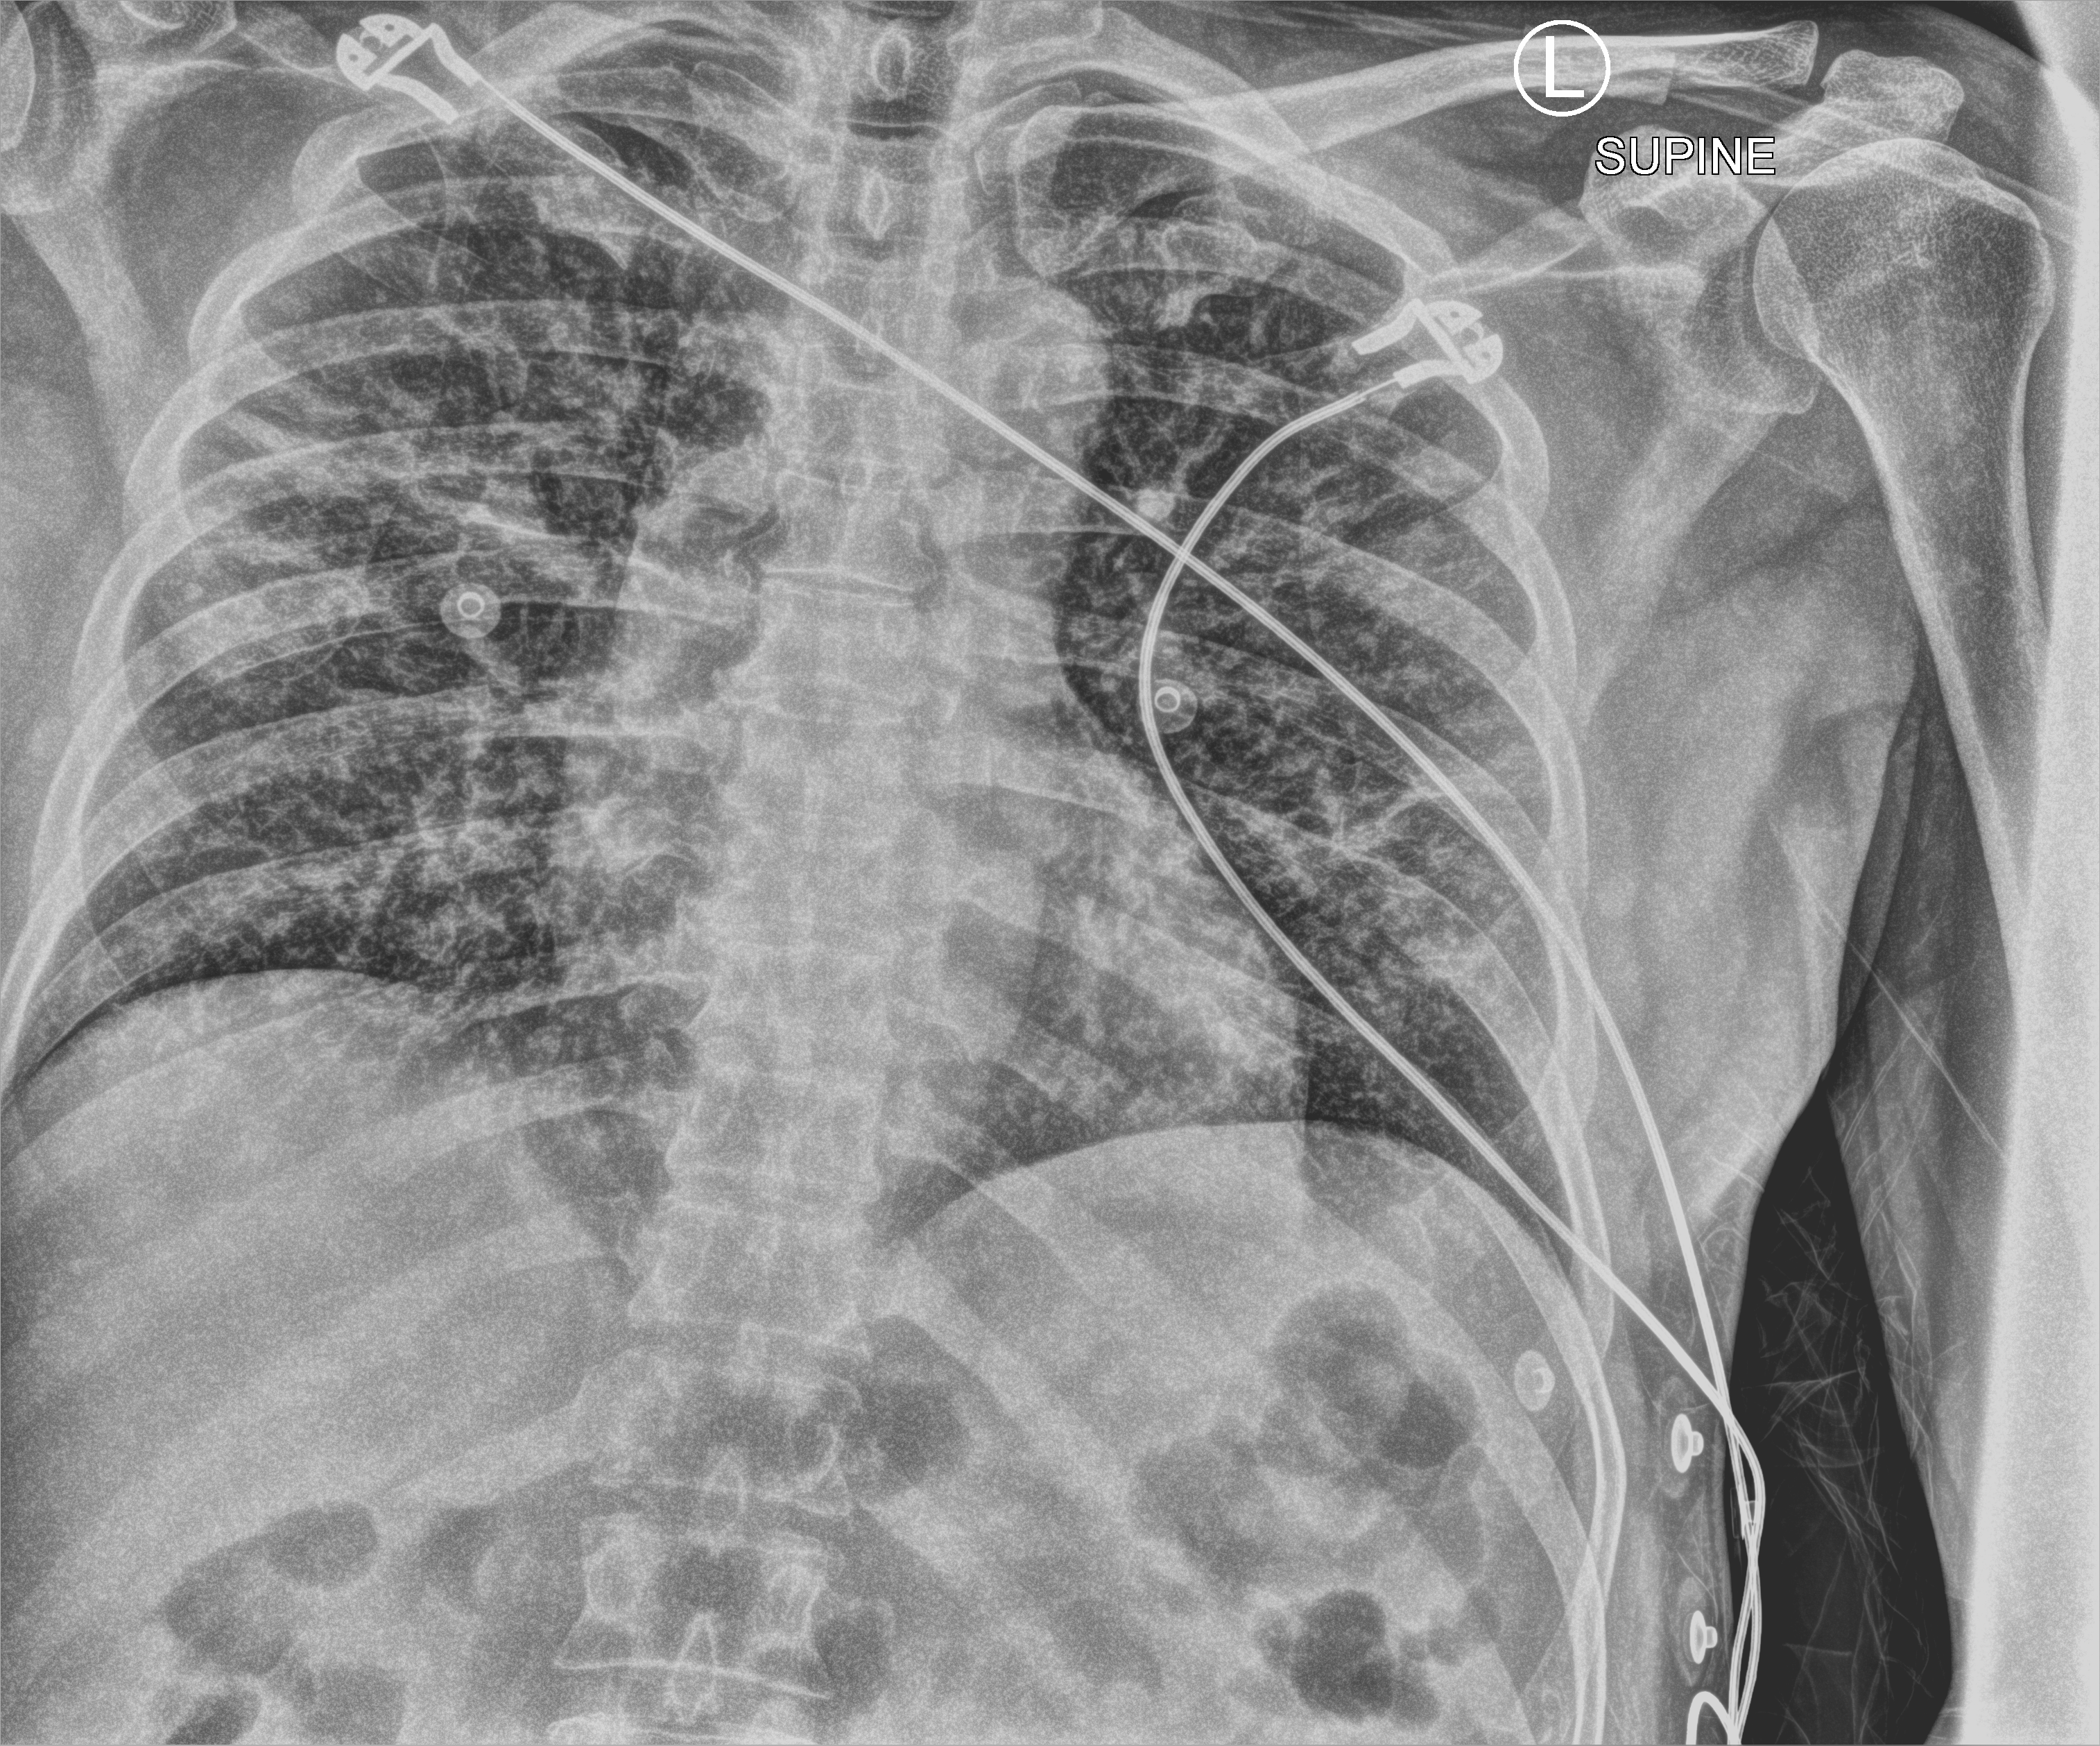
Chest X-ray (portable), anteroposterior (AP) projection. Male patient hospitalised with COVID-19, age 18–59 years.
Admission-level facts for this patient (not findings on this image; timing relative to this image not recorded): chronic kidney disease (admission record): no; mechanically ventilated during this hospital stay: no; admitted to intensive care during this hospital stay: no.